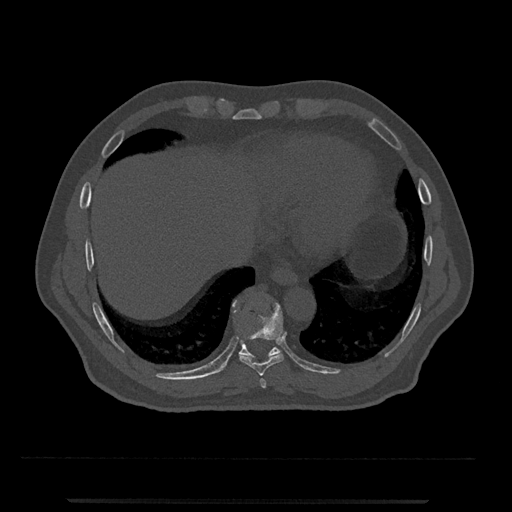
CT including the spine, one axial slice; position 553 of 797 along the scan axis; reconstruction kernel Br40s/3; 120 kVp; bone window (W 1800 / L 400 HU); 0.5 mm slice thickness; 512 × 512 image matrix, field of view 419 × 419 mm. Male patient, age 63 years. Case-level facts recorded for this patient, not image findings: primary cancer: prostate.
Structures marked on this image (semi-automatically segmented with operator editing):
- T10 vertebra: bounding box (x1, y1, x2, y2) in pixels: (222, 297, 281, 371)
- T8 vertebra: (260, 379, 267, 388)
- T9 vertebra: (239, 304, 284, 376)